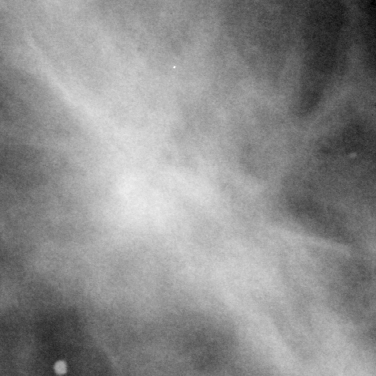
Crop from a digitized film mammogram around one marked abnormality, left breast, CC view.
- Mass, shape architectural distortion, margins spiculated; BI-RADS assessment category 4; pathology result (as recorded, not read from the image): benign.